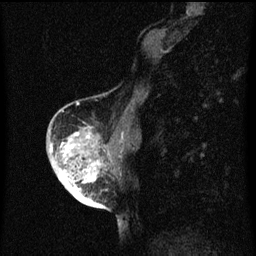
Breast MRI (dynamic contrast-enhanced), one sagittal slice. Slice 24 of 60 in the series (ordered by position). Dynamic contrast-enhanced series, image 2 of 3 at this slice position (ordered by acquisition). 1.5 T. TE 4.2 ms, TR 8 ms. 2 mm slice thickness. 256 × 256 image matrix, field of view 180 × 180 mm. Patient: female, 56 years.
Outlined on this slice (semi-automatically segmented with operator editing):
- analysis volume of interest (the breast-tissue region the enhancement analysis was run in; not a lesion): bounding box <54,122,118,199> (left, top, right, bottom; pixels)
- tumour enhancement mask (voxels above the 70 % enhancement threshold inside the analysis volume of interest): <59,132,101,199>